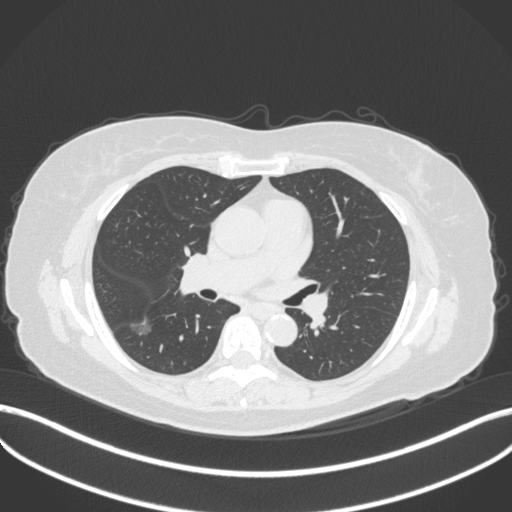
Chest CT, one axial slice; slice 177 of 322 in the series (ordered by position); reconstruction kernel B31f; 120 kVp; lung window (W 1500 / L -600 HU); 1 mm slice thickness; 512 × 512 image matrix, field of view 400 × 400 mm. Female patient, age 64 years. From the clinical record (not read from this slice): clinical TNM (as recorded): T1c N0 M0; histopathological grade: G1.
Outlined on this slice (rectangle marked by the reading radiologist):
- lung tumour (recorded histology: adenocarcinoma): bounding box [x1, y1, x2, y2] px = [129, 316, 154, 339]